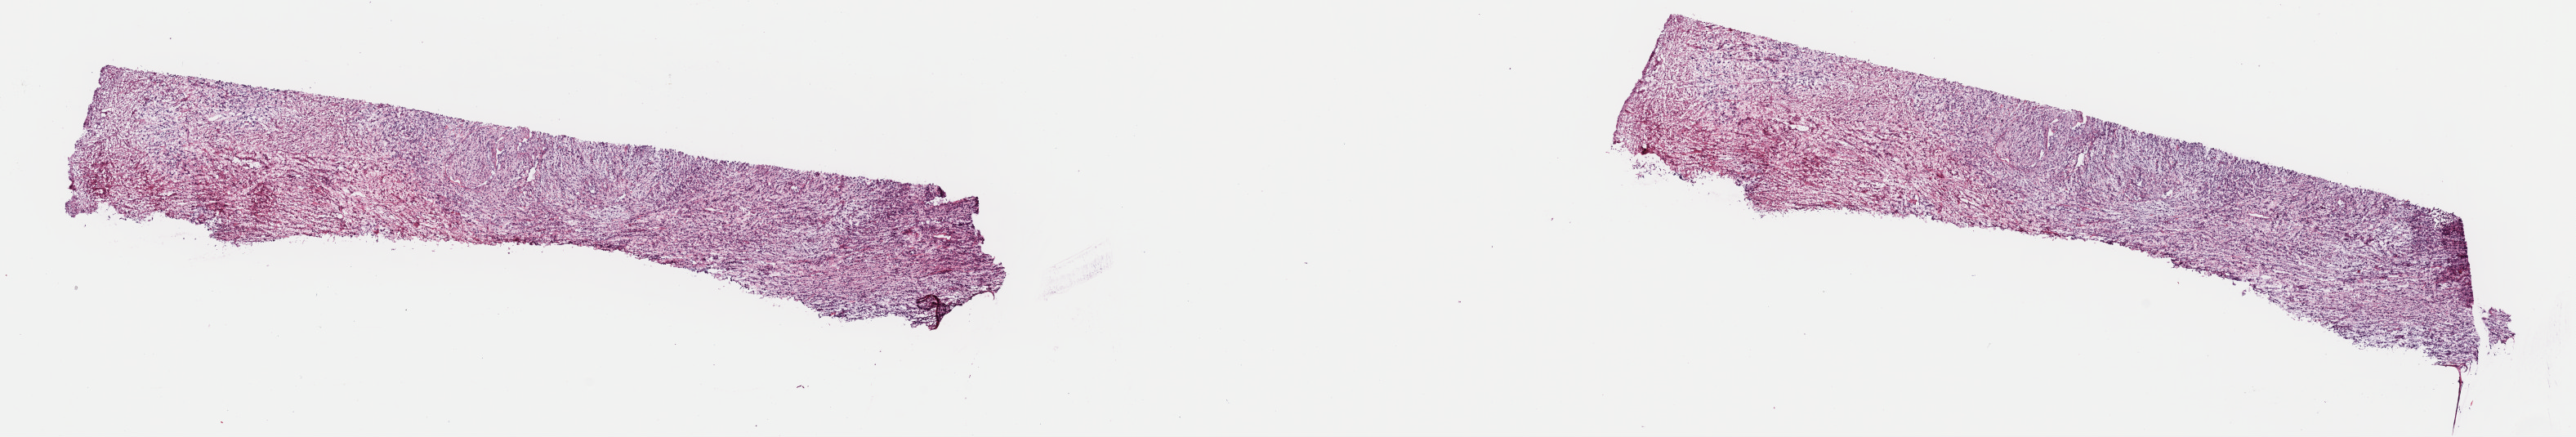
Digitized H&E tissue section (whole slide) — low-resolution overview of the scanned area, about 24.9 x 4.2 mm, frozen section from the top of the tissue portion, connective, subcutaneous and other soft tissues, primary tumour sample. Patient: female, age at initial diagnosis 86 years. Composition of this section per pathologist review: tumour cells 95%, tumour nuclei 80%, normal cells 0%, stromal cells 0%, necrosis 5%. Infiltration values recorded for this section: lymphocyte infiltration 2%, monocyte infiltration 0%, neutrophil infiltration 0%.
Diagnosis: Fibromyxosarcoma (connective, subcutaneous and other soft tissues of pelvis).